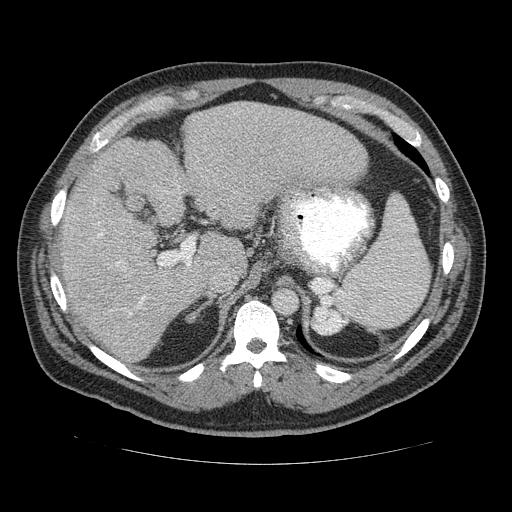
Contrast-enhanced abdominal CT (liver protocol), one axial slice. Position 88 of 113 along the scan axis. Soft-tissue window (W 400 / L 40 HU). 2.5 mm slice thickness. 512 × 512 image matrix. From the clinical record (not read from this slice): diagnosis: hepatocellular carcinoma (patient treated with transarterial chemoembolisation; whether this scan precedes or follows treatment is not stated here); TNM stage (as recorded): Stage-II; Child-Pugh class: B; tumour differentiation: moderately differentiated; tumour nodularity: multinodular.
Structures marked on this image (semi-automatically segmented with operator editing):
- liver parenchyma outside the tumour (the mass and vessels are separate outlines, so this box may not span the whole liver): bounding box <52,102,370,362> (left, top, right, bottom; pixels)
- liver vessels: <60,191,192,313>